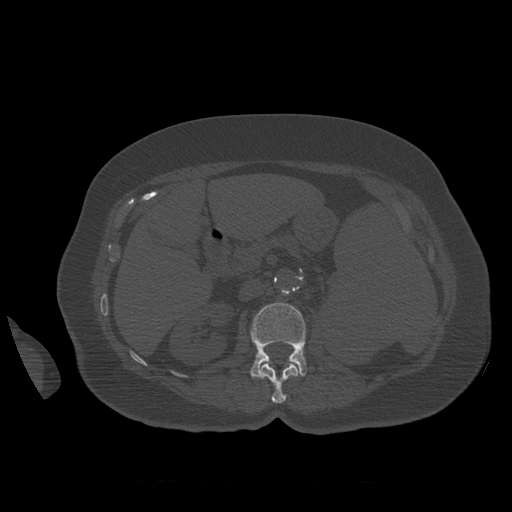
CT including the spine, one axial slice. Reconstruction kernel STANDARD. 120 kVp. Bone window (W 1800 / L 400 HU). 512 × 512 image matrix. Patient age 81 years. From the clinical record (not read from this slice): primary cancer: renal.
Outlined on this slice (semi-automatically segmented with operator editing):
- L1 vertebra: bounding box (x1, y1, x2, y2) in pixels: (259, 363, 299, 404)
- L2 vertebra: (250, 303, 307, 378)